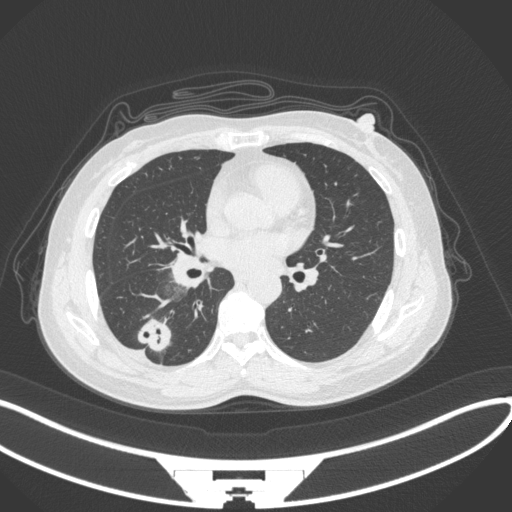
Chest CT, one axial slice; slice 146 of 352 in the series (ordered by position); reconstruction kernel B31f; 120 kVp; lung window (W 1500 / L -600 HU); 1 mm slice thickness; 512 × 512 image matrix, field of view 400 × 400 mm. Patient: female, 55 years. Case-level facts recorded for this patient, not image findings: clinical TNM (as recorded): T1c N1 M0.
Structures marked on this image (bounding box drawn by a radiologist):
- lung tumour (recorded histology: adenocarcinoma): box from (x=133, y=315) to (x=174, y=353) px